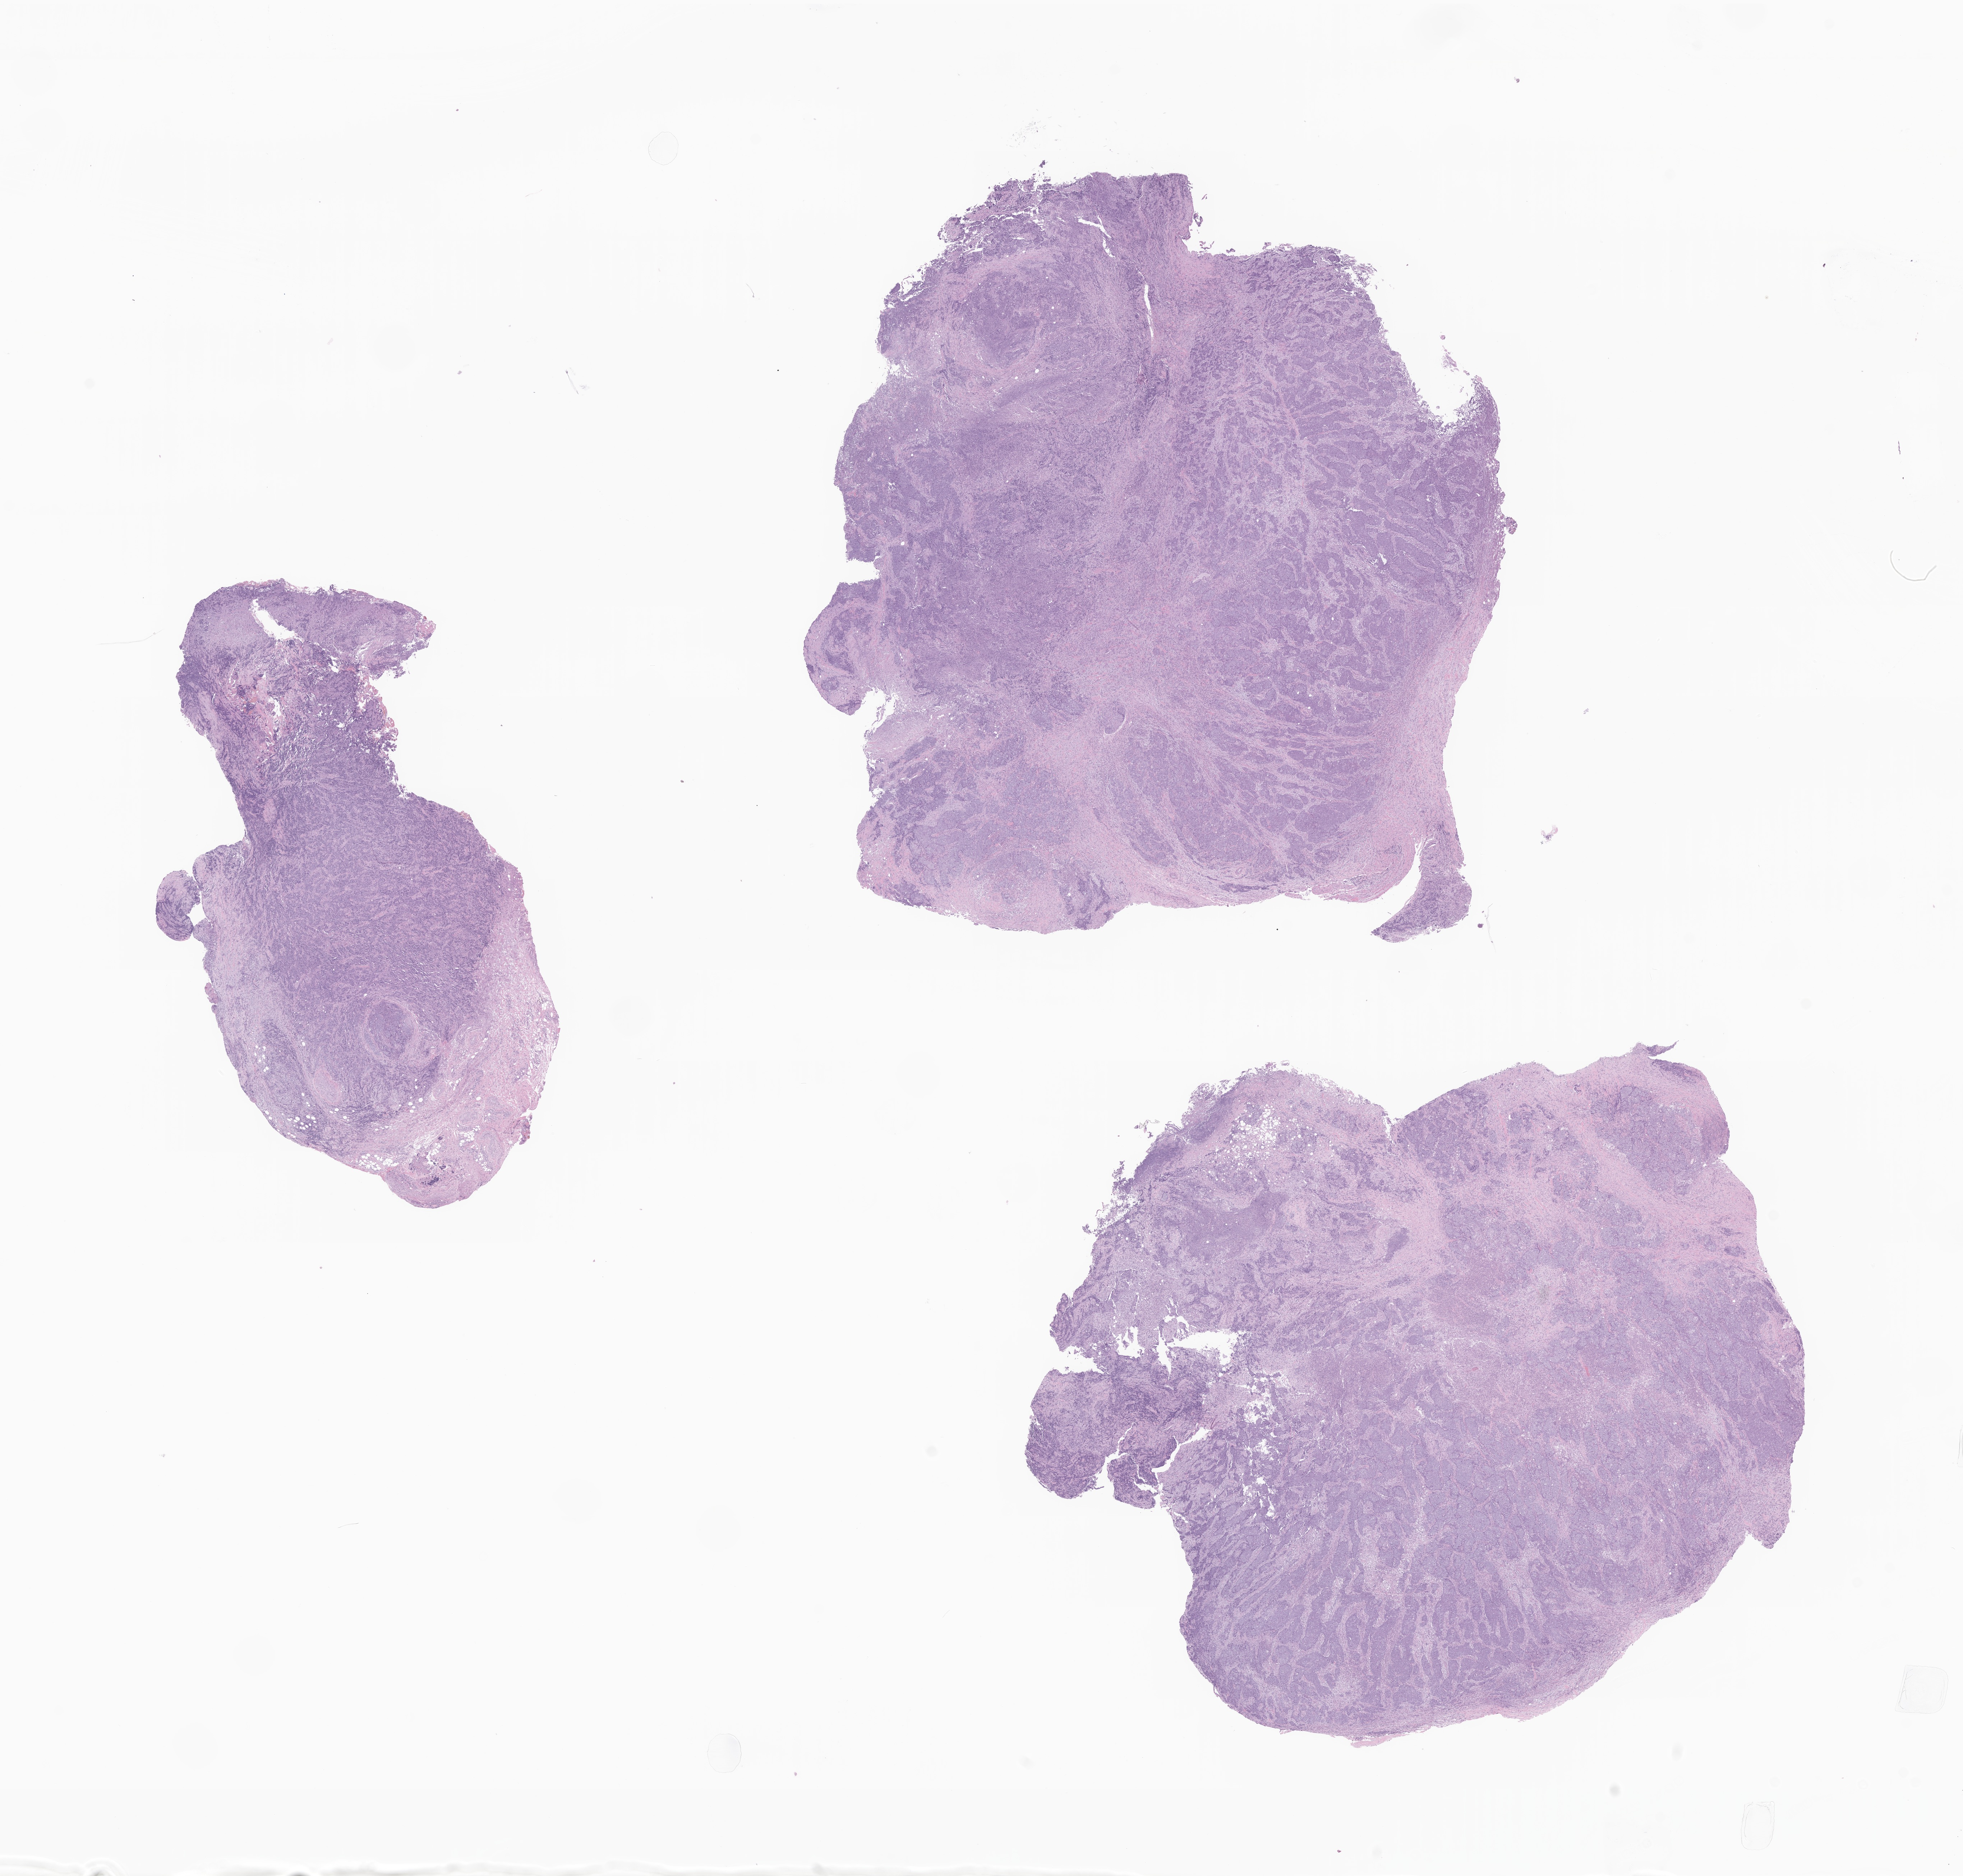
Whole-slide image, haematoxylin and eosin stain of tumor tissue from the thyroid, whole scanned area (about 23.0 x 22.0 mm) shown as a low-resolution overview. Formalin-fixed paraffin-embedded section. Female patient, age 215 months.
Diagnosis: Carcinoma, NOS.